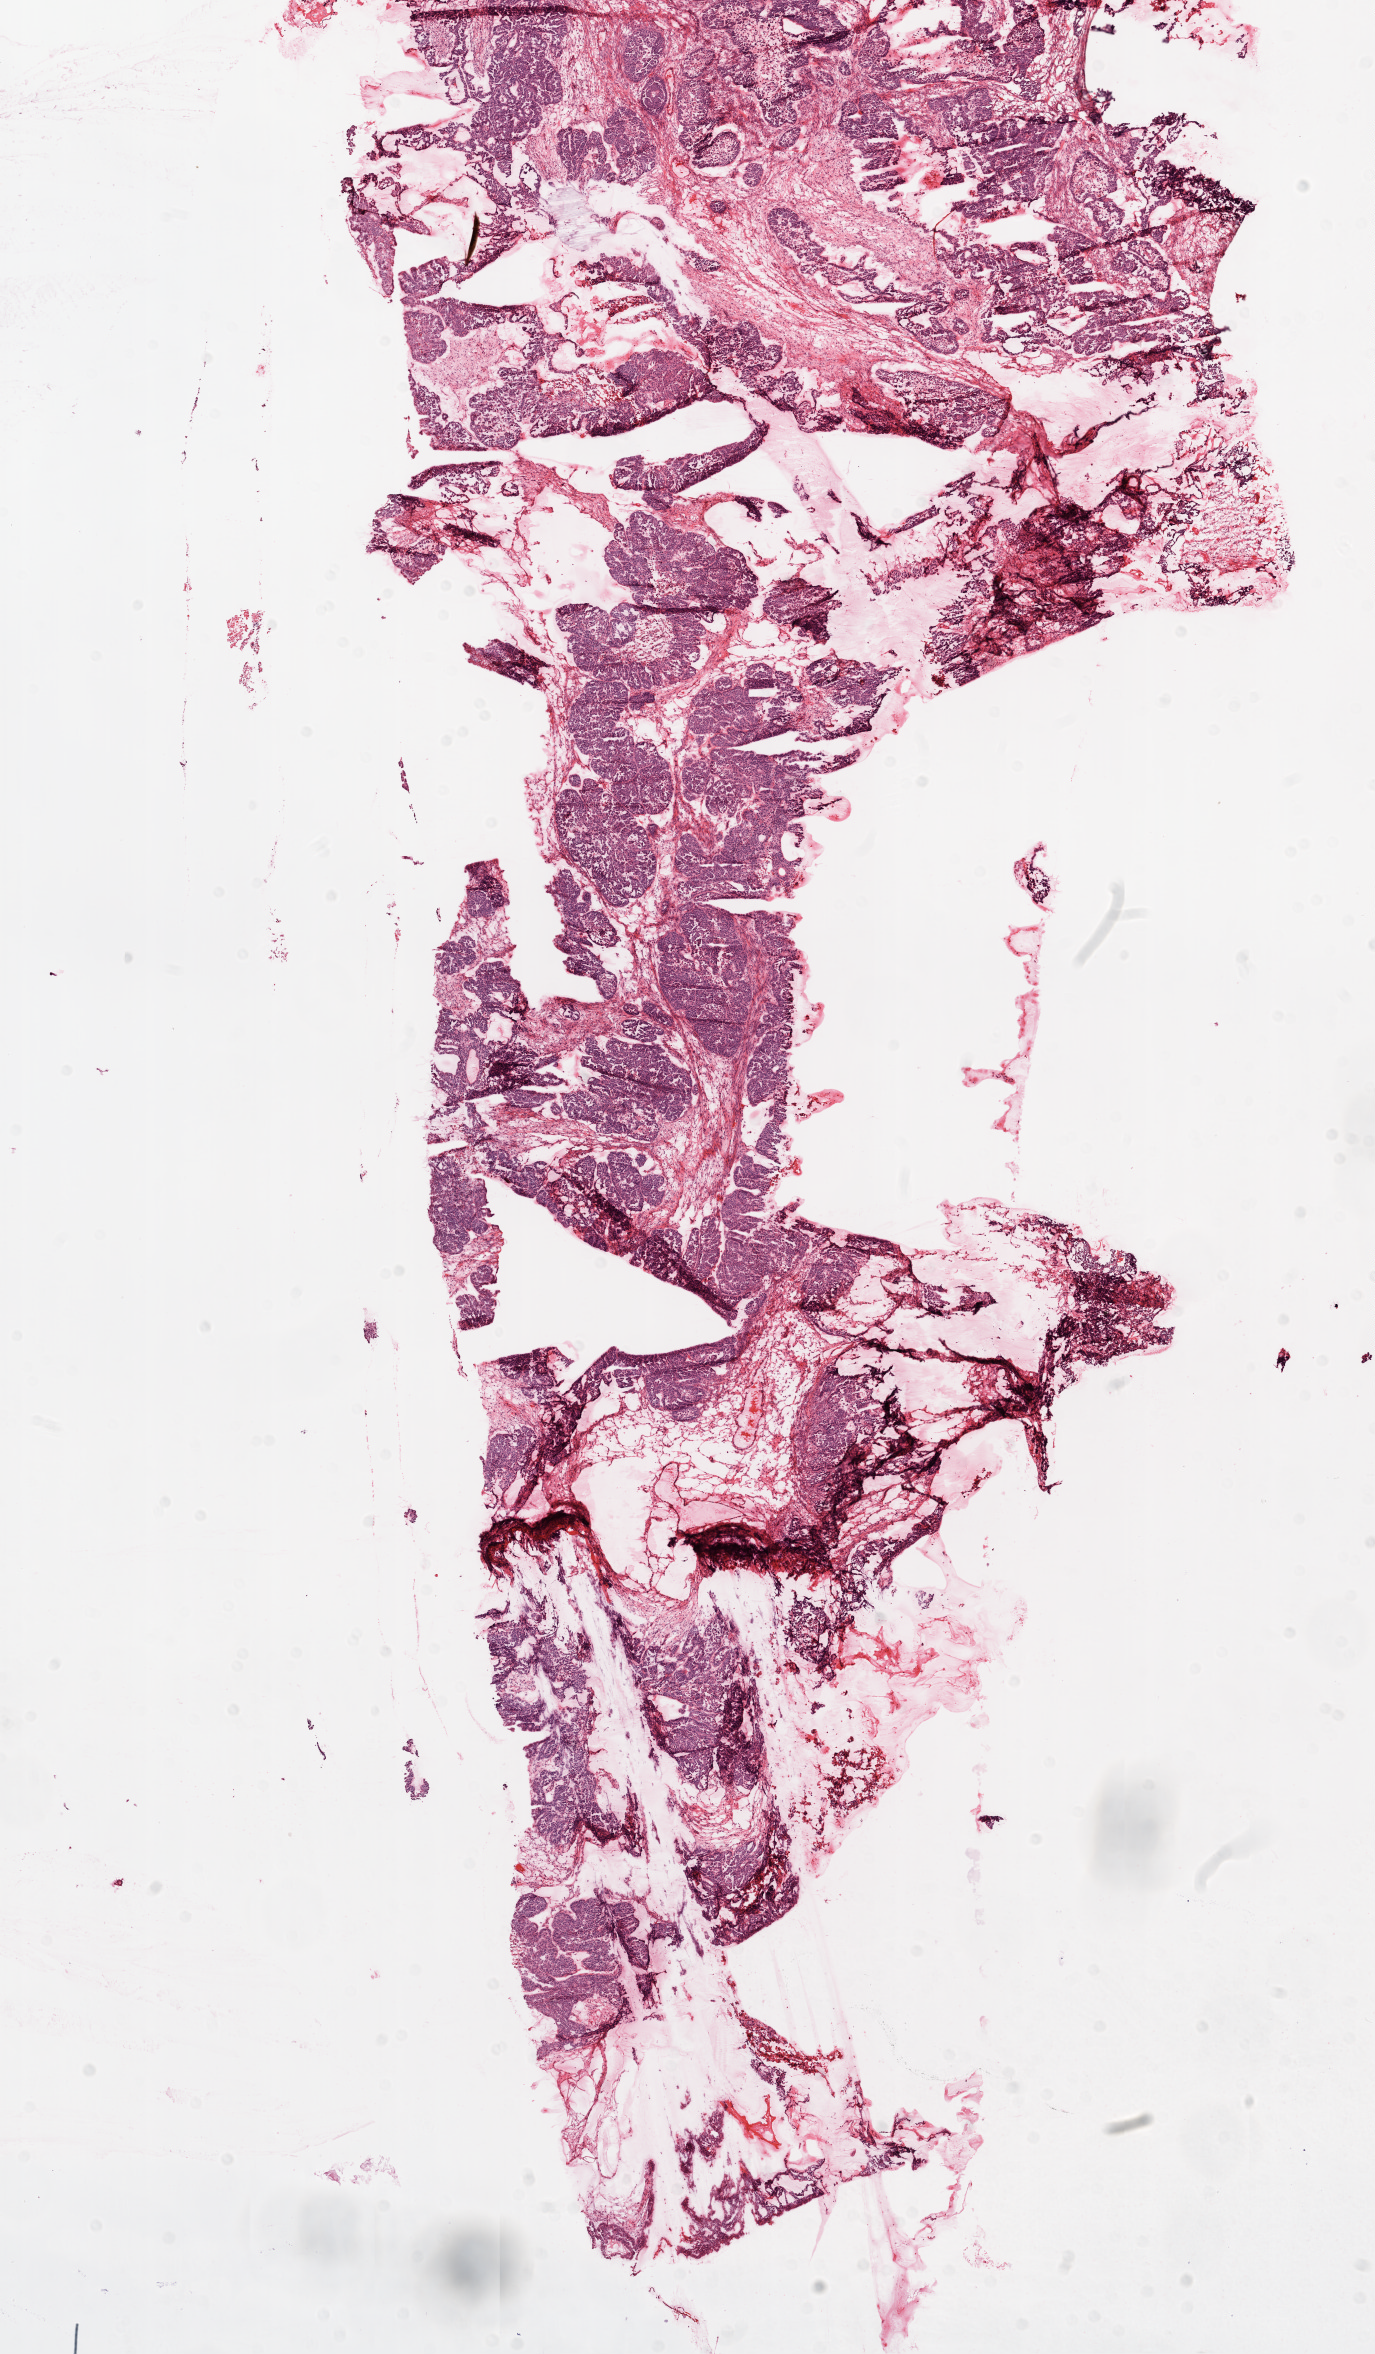
Whole-slide histology image, Hematoxylin and eosin (H&E) stained, low-resolution overview of the scanned area, about 11.0 x 18.9 mm, frozen section, ovary, primary tumour sample. Patient: female, age at initial diagnosis 62 years. Histologic grade: G2 (moderately differentiated). Pathologist review of this section (percent, as recorded): tumour cells 70%, tumour nuclei 70%, normal cells 0%, stromal cells 30%, necrosis 0%.
* FIGO stage: IIIC
* histologic diagnosis: Serous cystadenocarcinoma, NOS